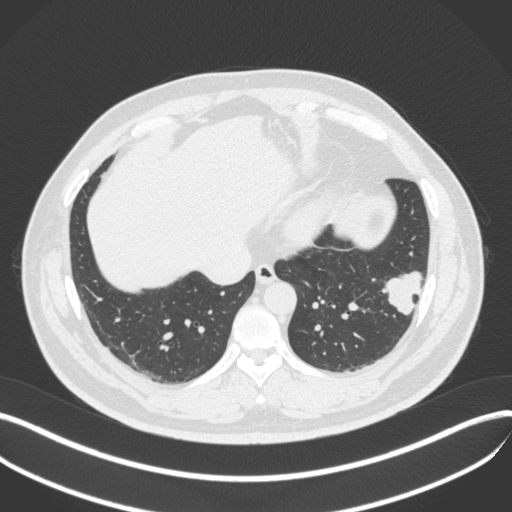
Chest CT, one axial slice. Slice 125 of 420 in the series (ordered by position). Reconstruction kernel B31f. 120 kVp. Lung window (W 1500 / L -600 HU). 1 mm slice thickness. 512 × 512 image matrix. Patient: male, 39 years. Case-level facts recorded for this patient, not image findings: clinical TNM (as recorded): T2a N0 M0; histopathological grade: G2-3.
Outlined on this slice (rectangle marked by the reading radiologist):
- lung tumour (recorded histology: adenocarcinoma): bounding box (x1, y1, x2, y2) in pixels: (380, 264, 426, 319)